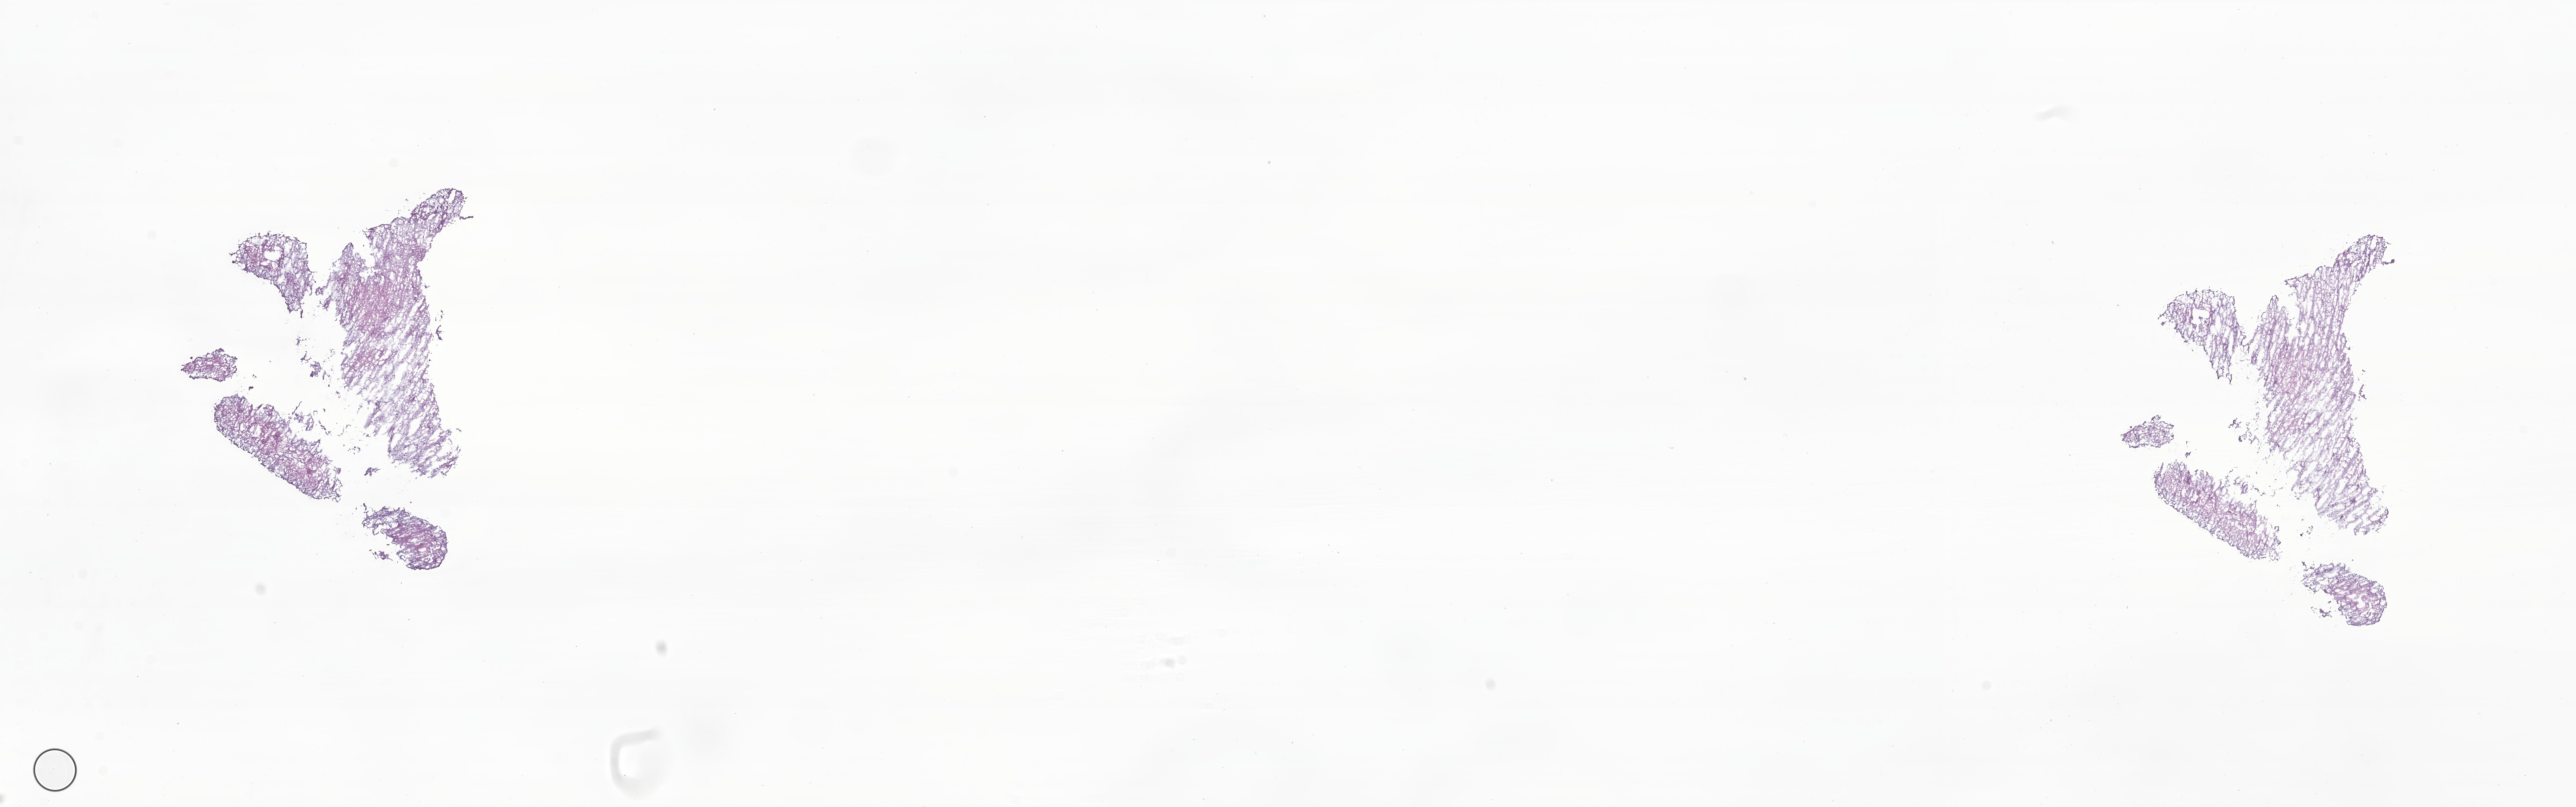
Haematoxylin and eosin whole-slide image of tumor tissue from the brain — shown as a low-resolution overview of the whole scanned area (about 27.3 x 8.5 mm). Frozen section. Patient male; age 730 days.
- recorded diagnosis: Pilocytic astrocytoma